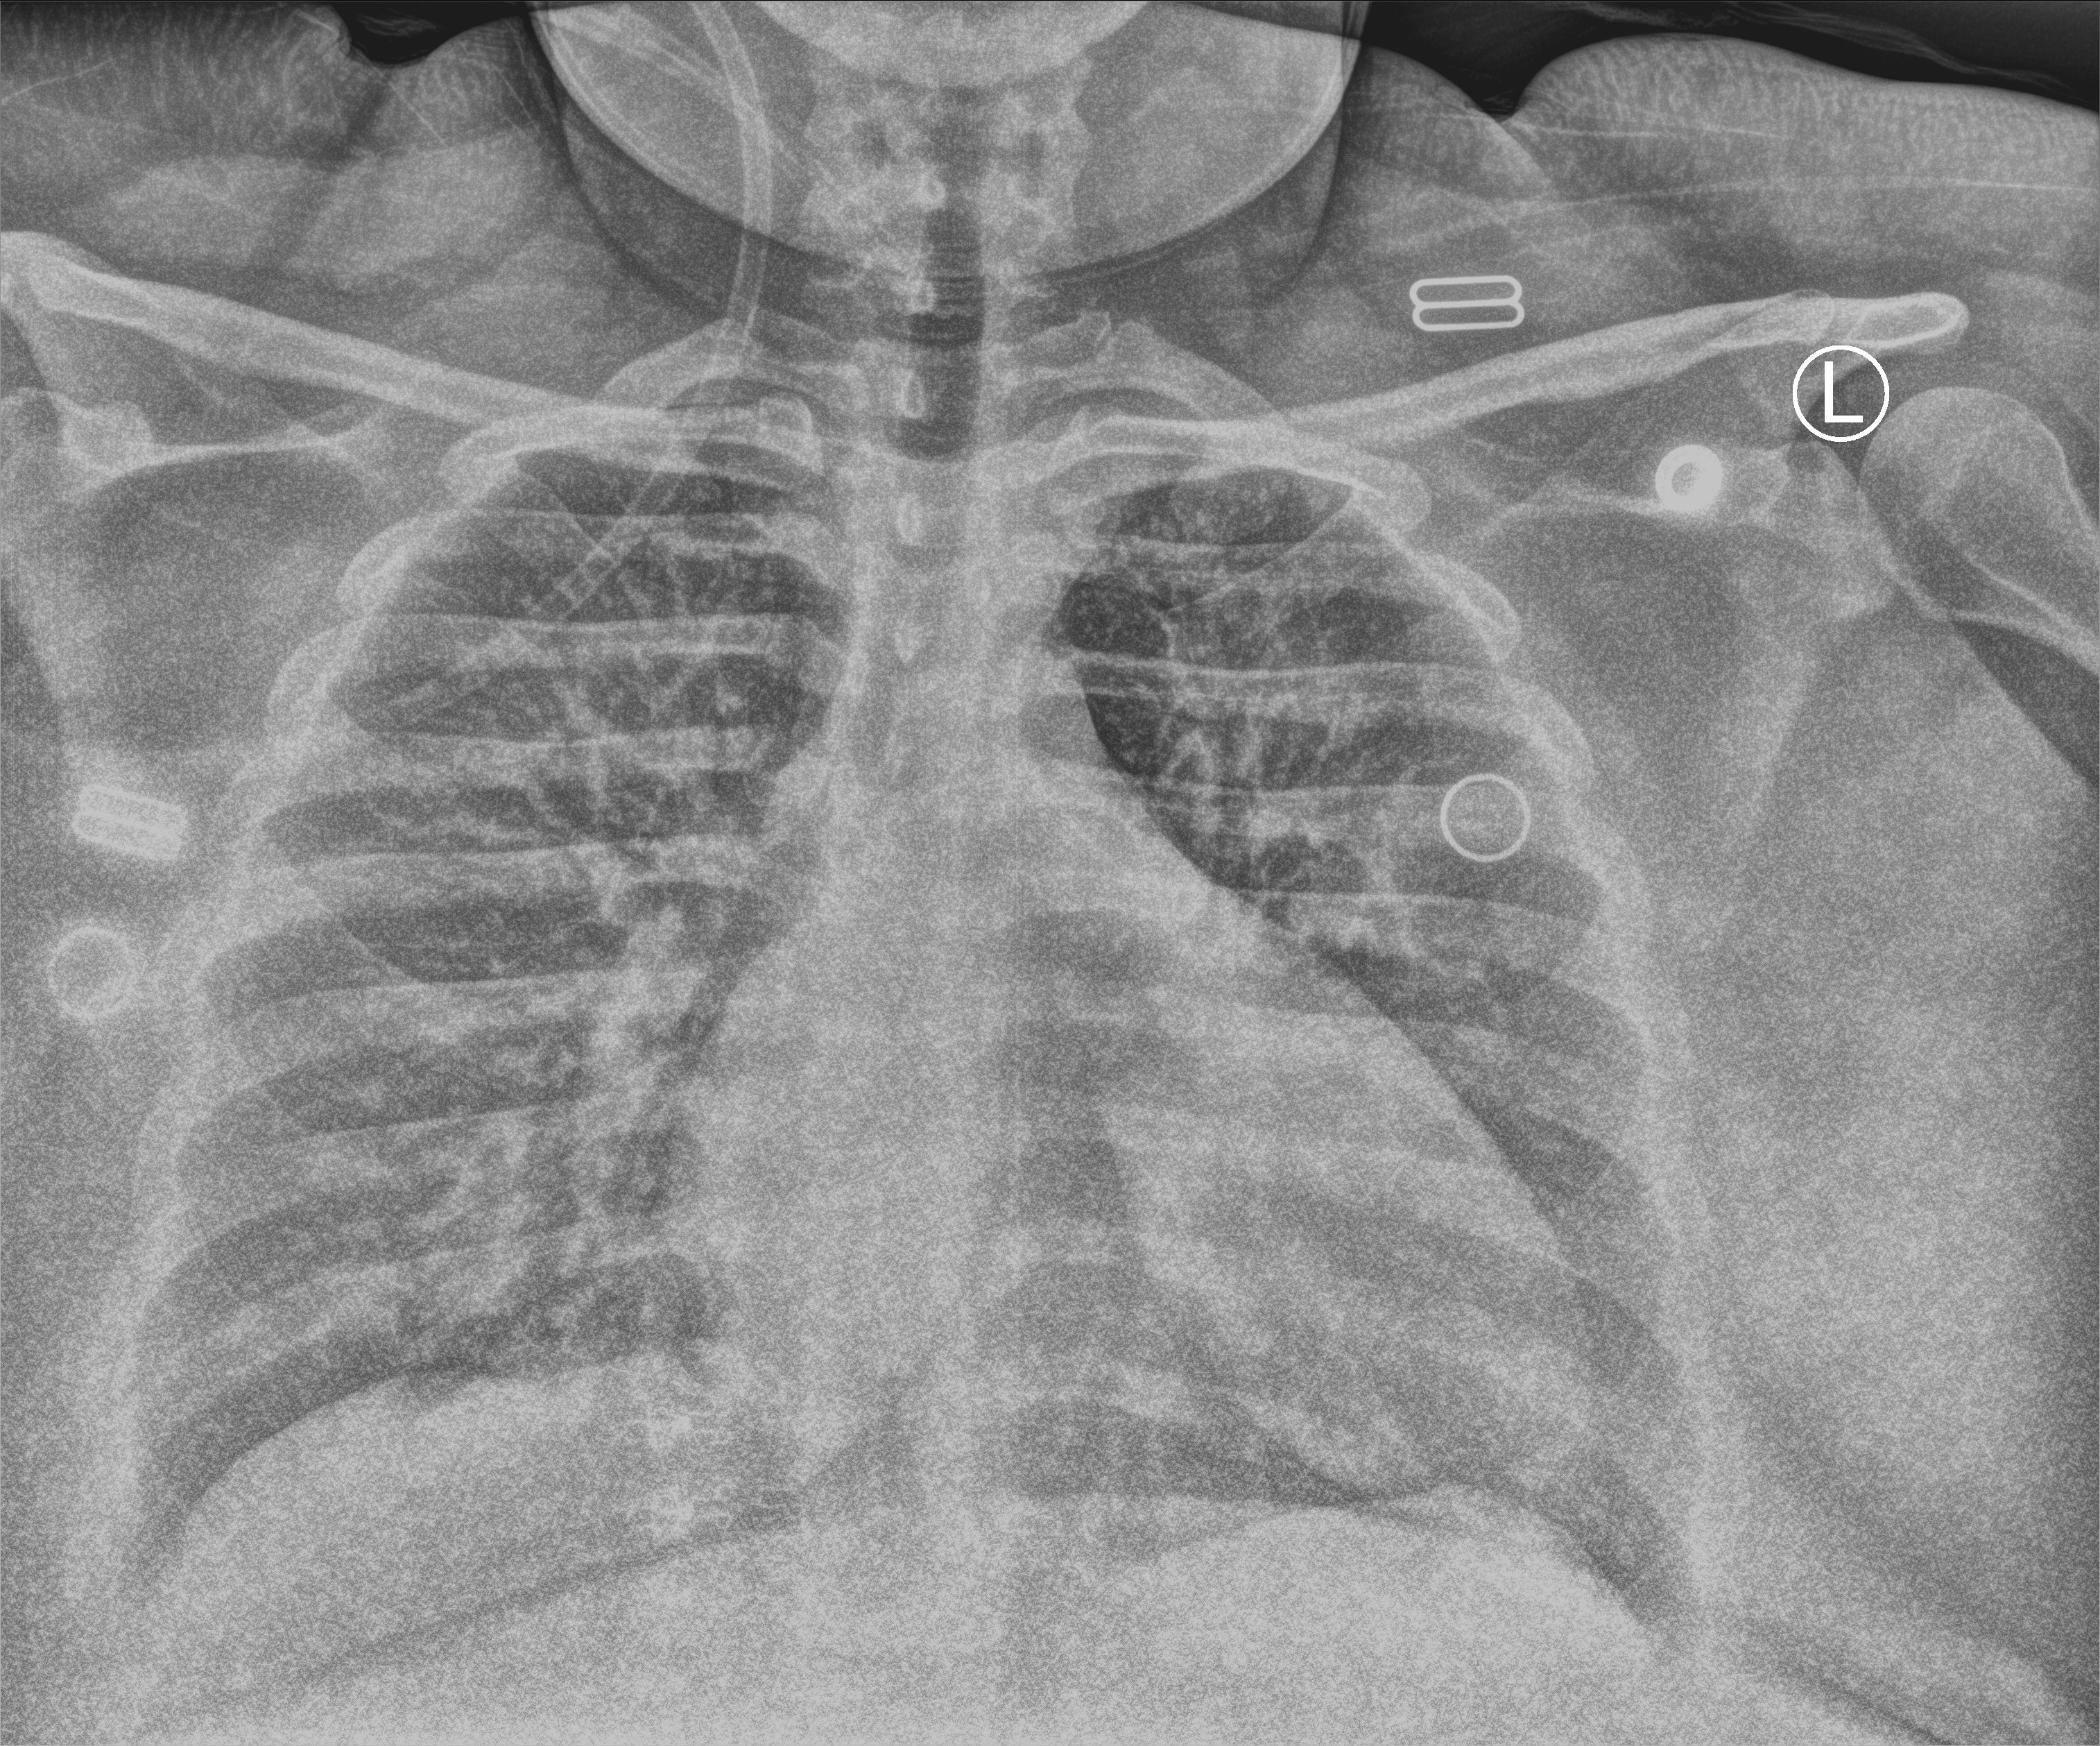
Bedside chest radiograph (computed radiography); anteroposterior (AP) projection. Female patient hospitalised with COVID-19, age 18–59 years.
From the hospital-stay record, not from the radiograph (when in the stay this image was taken is not recorded): admitted to intensive care during this hospital stay: no.